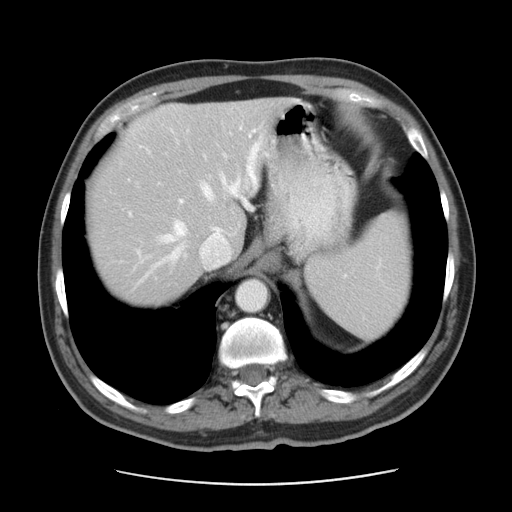
Contrast-enhanced abdominal CT, one axial slice. Position 34 of 42 along the scan axis. Reconstruction kernel STANDARD. Intravenous contrast given. Soft-tissue window (W 400 / L 40 HU). 5 mm slice thickness. 512 × 512 image matrix, field of view 370 × 370 mm. Male patient, age 73 years. From the clinical record (not read from this slice): diagnosis: colorectal cancer liver metastases, imaged before liver resection; multiple liver metastases: yes; largest metastasis: 0.5 cm; disease in both lobes: no.
Outlined on this slice (expert manual segmentation):
- hepatic veins: box from (x=137, y=144) to (x=258, y=285) px
- liver: (x=89, y=98)–(x=285, y=303)
- planned liver remnant (the part of the liver to remain after resection): (x=123, y=98)–(x=285, y=249)
- portal vein (with intrahepatic branches): (x=129, y=126)–(x=262, y=215)